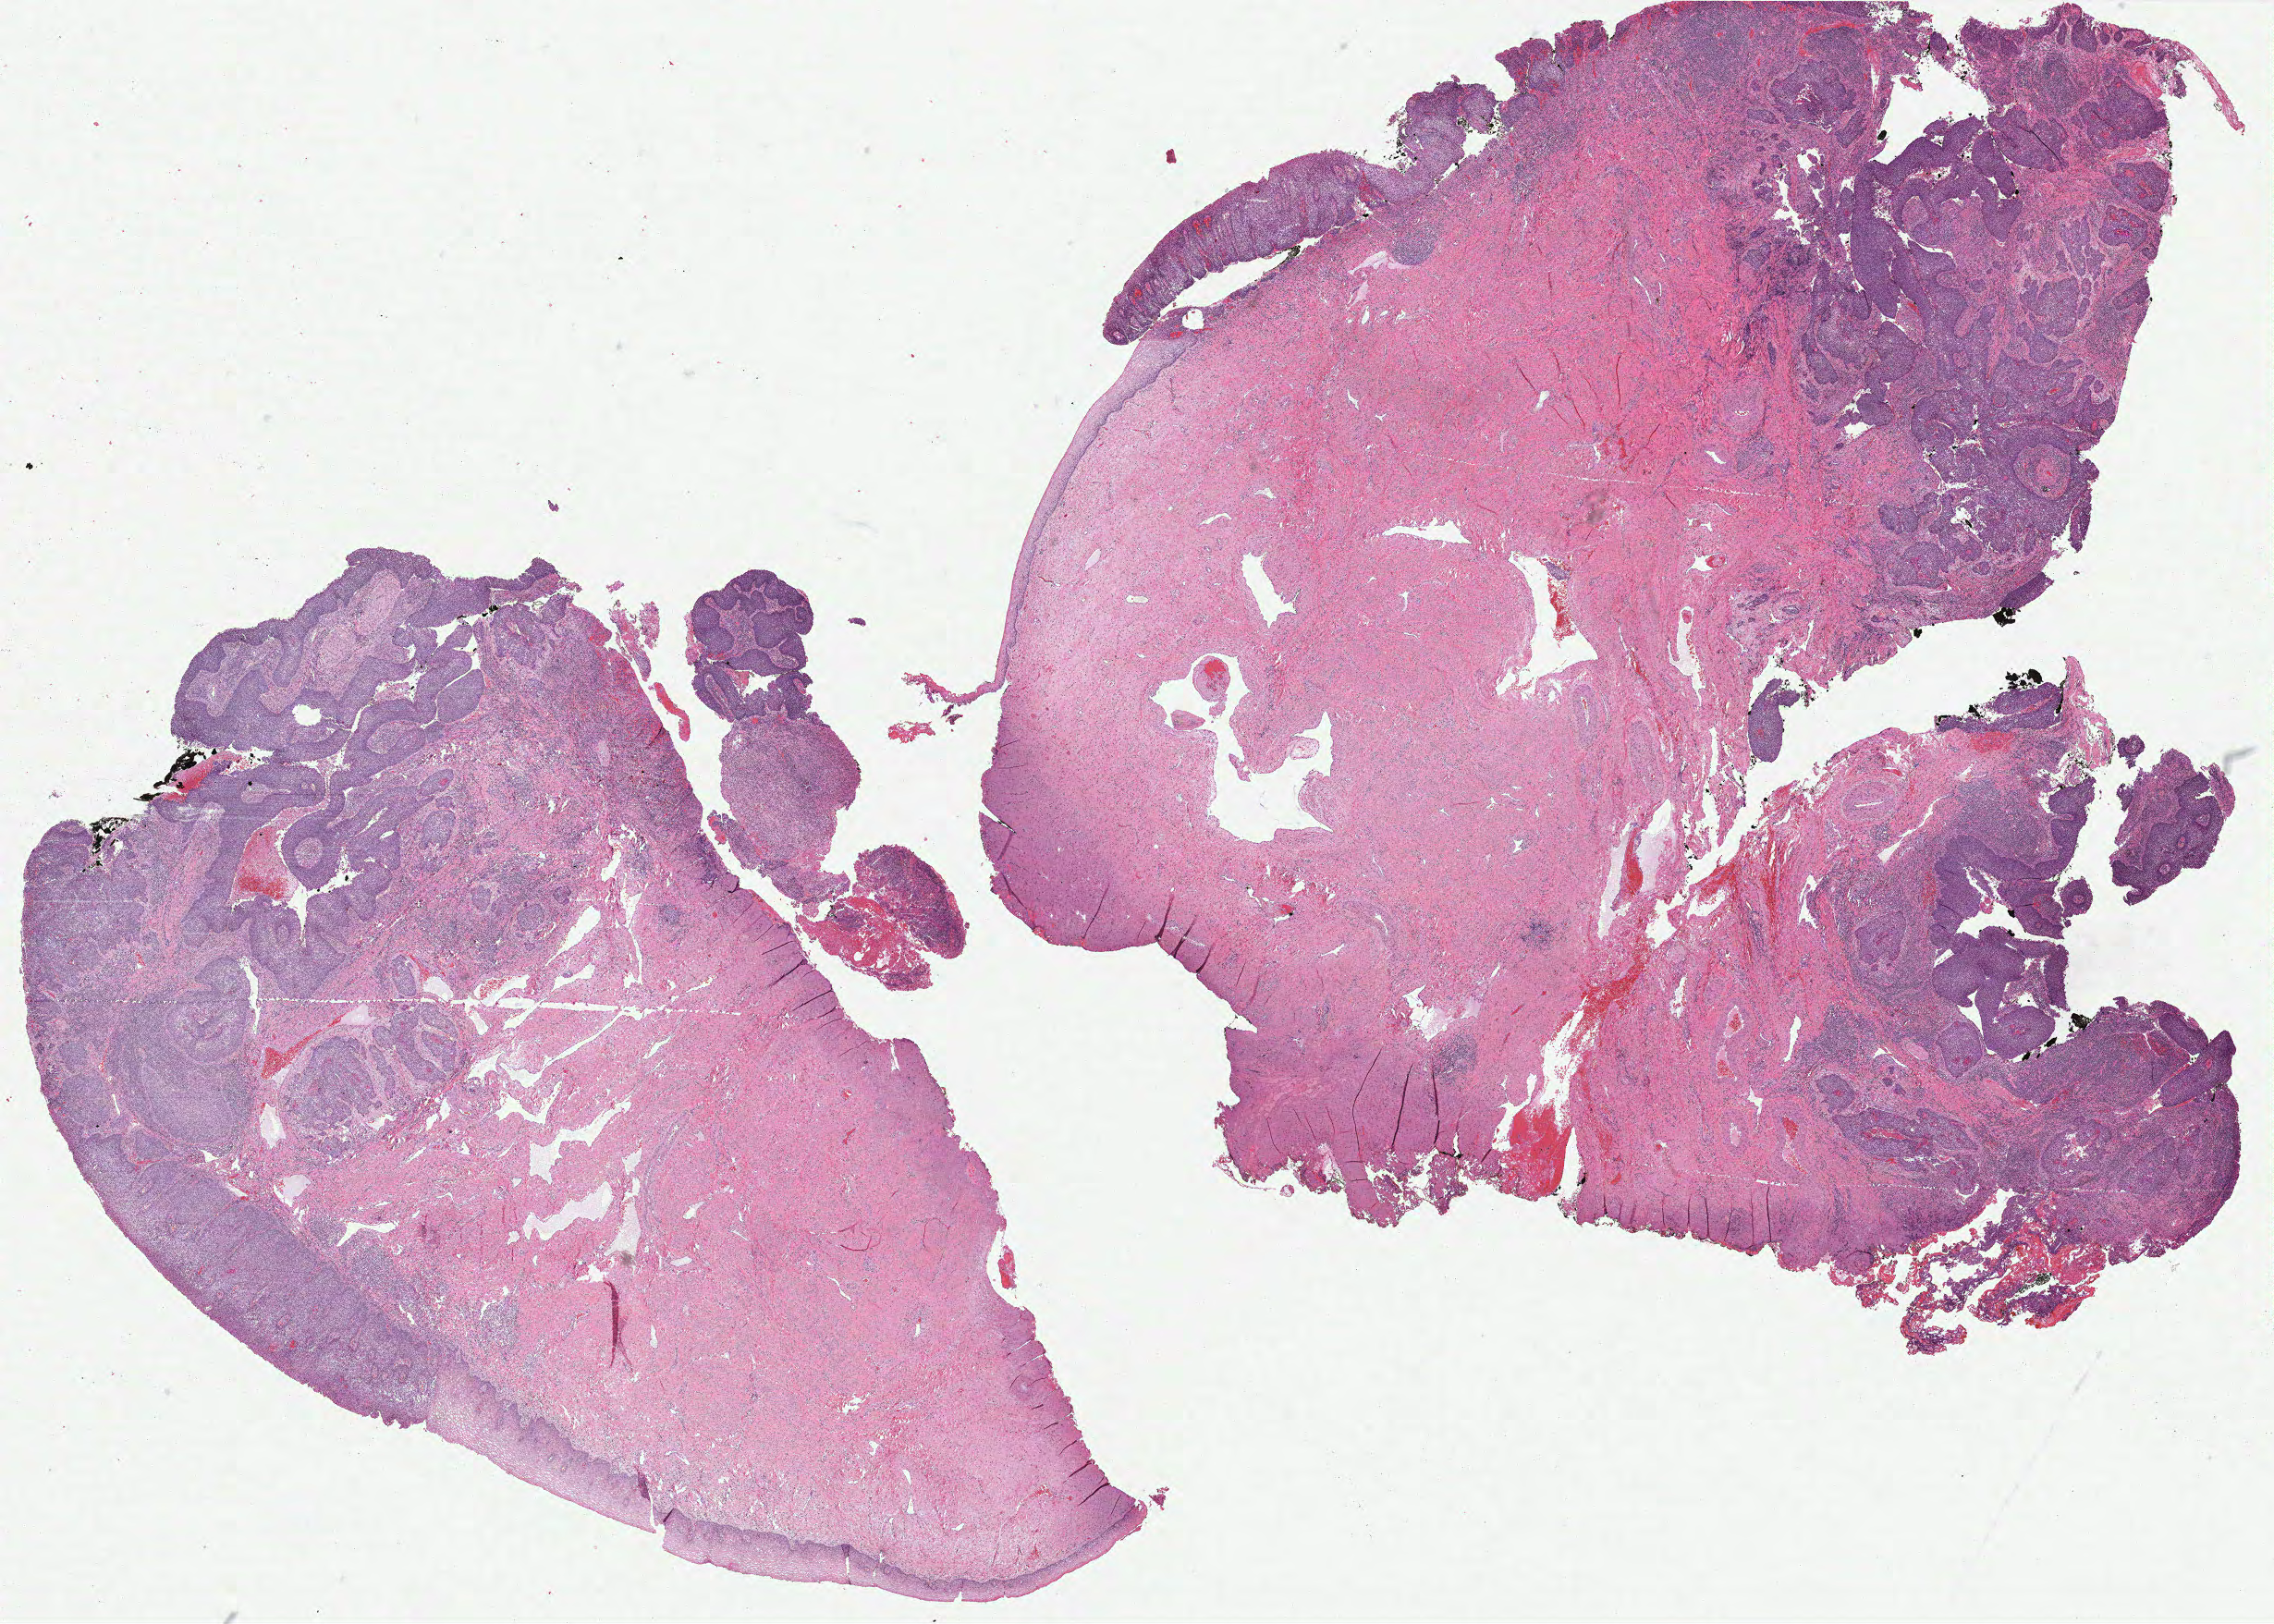
Whole-slide histology image, H&E-stained, whole scanned area (about 19.7 x 14.1 mm, slide scanned at 40x) shown as a low-resolution overview, formalin-fixed paraffin-embedded (FFPE) diagnostic section, cervix, primary tumour sample. Patient: female, age at initial diagnosis 41 years. Histologic grade: G2 (moderately differentiated).
• diagnosis: Squamous cell carcinoma, keratinizing, NOS (cervix uteri)
• FIGO stage: IIB